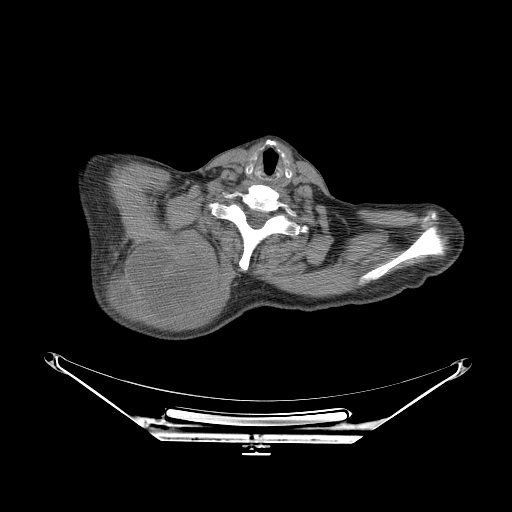
CT of an extremity soft-tissue mass (from a PET/CT study), one axial slice. Slice 213 of 267 in the series (ordered by position). 140 kVp. Soft-tissue window (W 400 / L 40 HU). 512 × 512 image matrix, field of view 500 × 500 mm. Male patient. Case-level facts recorded for this patient, not image findings: histological type: pleiomorphic spindle cell undifferentiated; grade: high; site of the primary tumour: right parascapusular.
Outlined on this slice (expert contour drawn on MRI and transferred to this co-registered scan by the dataset authors):
- gross tumour volume including surrounding oedema: bounding box [x1, y1, x2, y2] px = [107, 235, 231, 323]
- gross tumour volume (mass): [128, 238, 215, 318]